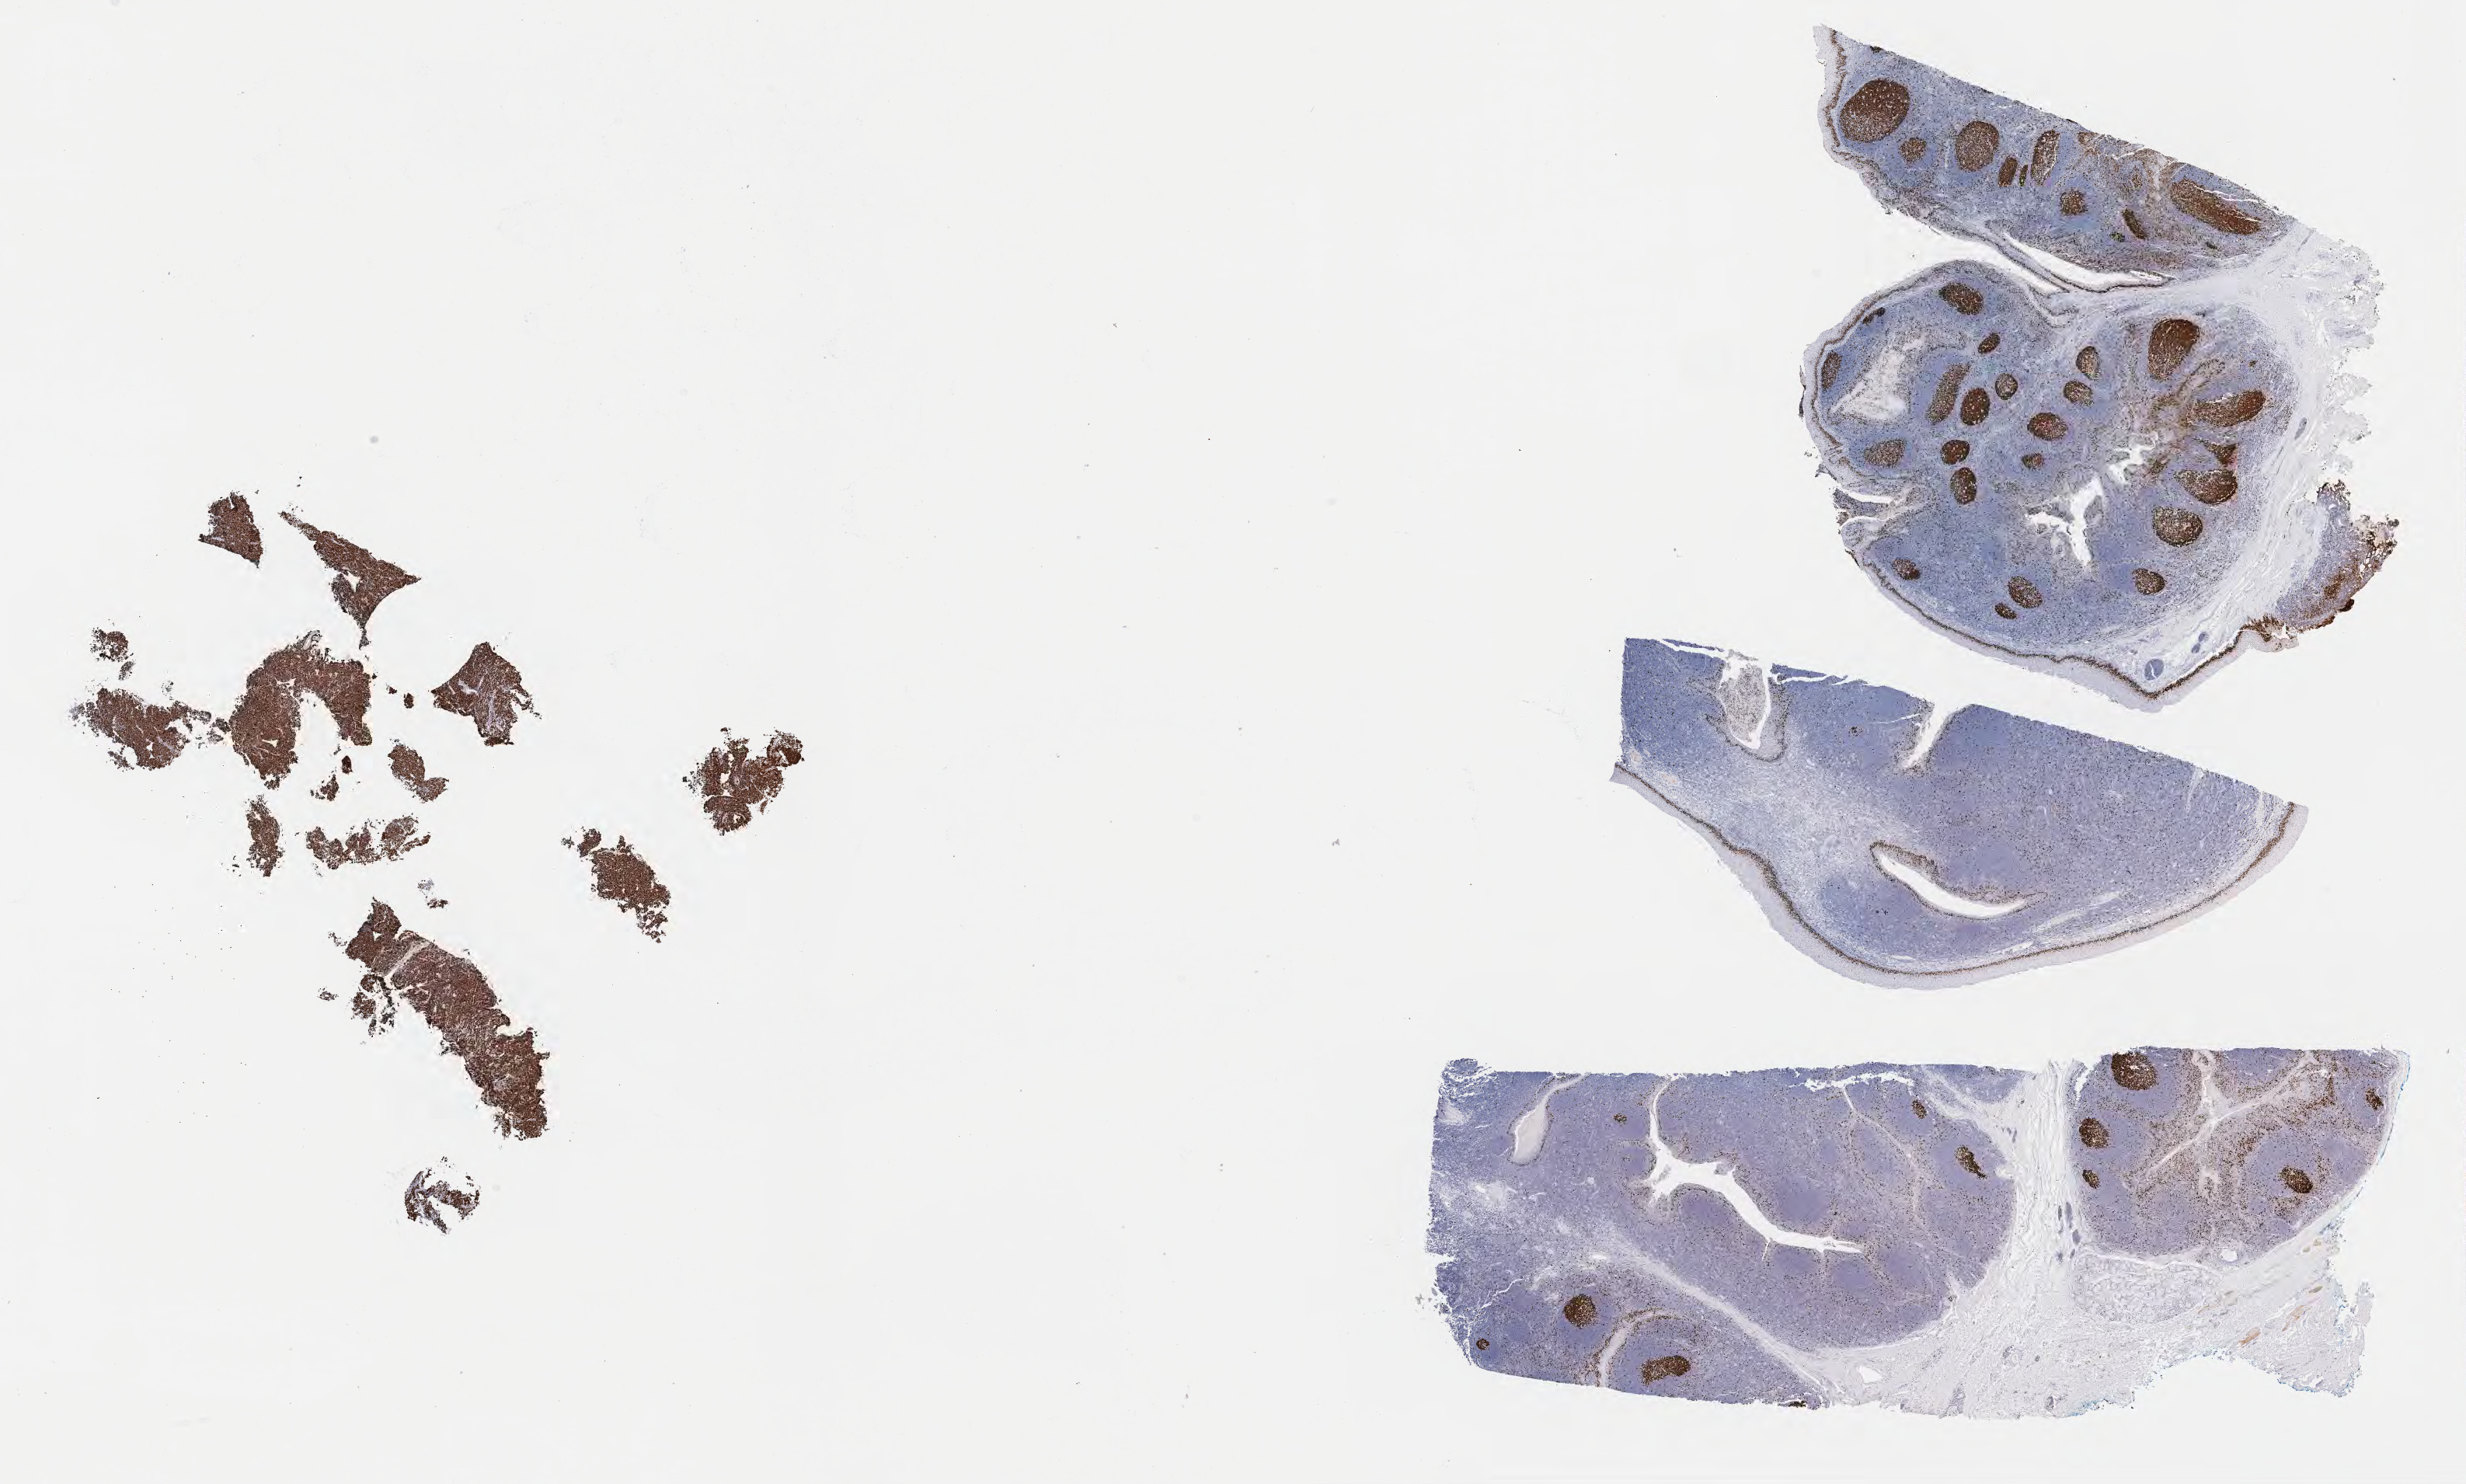
Whole-slide image, immunohistochemical stain for Ki-67, whole scanned area (about 25.7 x 15.4 mm) shown as a low-resolution overview, specimen: tumor tissue, site: kidney. Patient: female, age at initial diagnosis 8 years.
Diagnosis: Burkitt lymphoma, NOS.